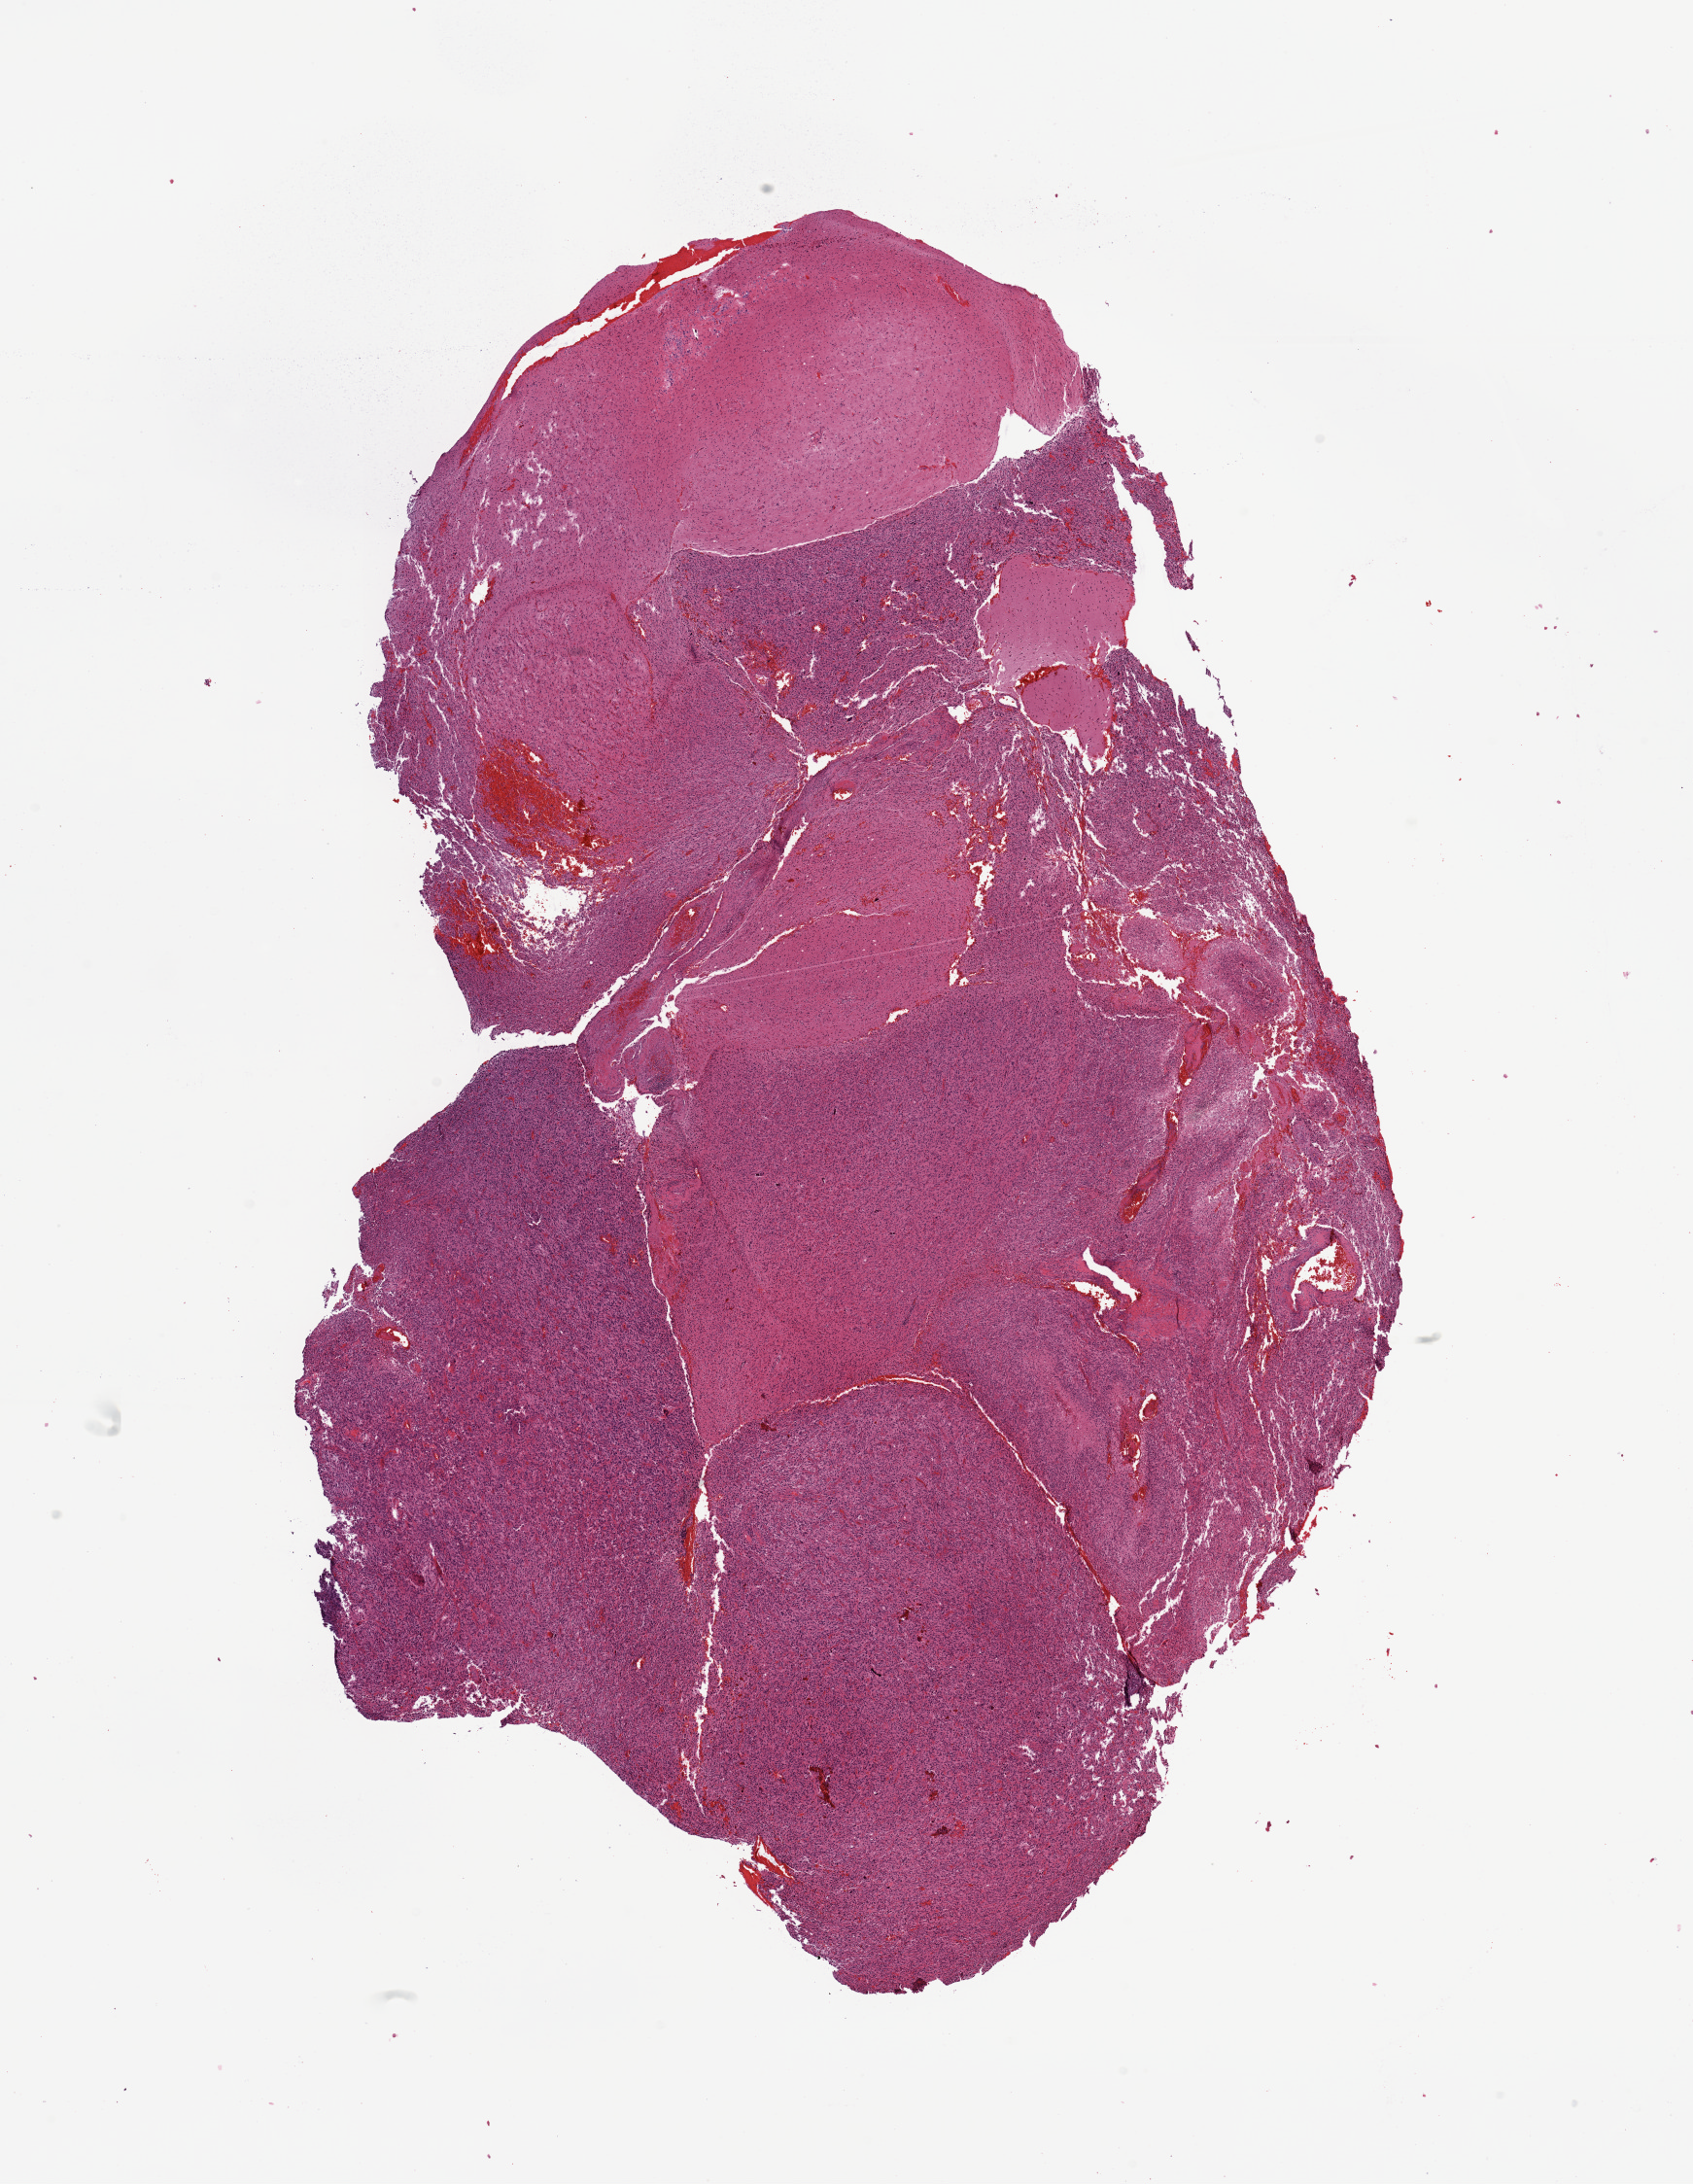
Digitized Hematoxylin and eosin (H&E) stained tissue section (whole slide), whole scanned area (about 13.8 x 17.8 mm) shown as a low-resolution overview; tumour tissue sample, sampled site: brain. 58-year-old male patient. Composition of this section per pathologist review: tumour nuclei 85%, necrosis 5%.
Primary tumour site (as recorded): temporal lobe. Diagnosis: Glioblastoma.